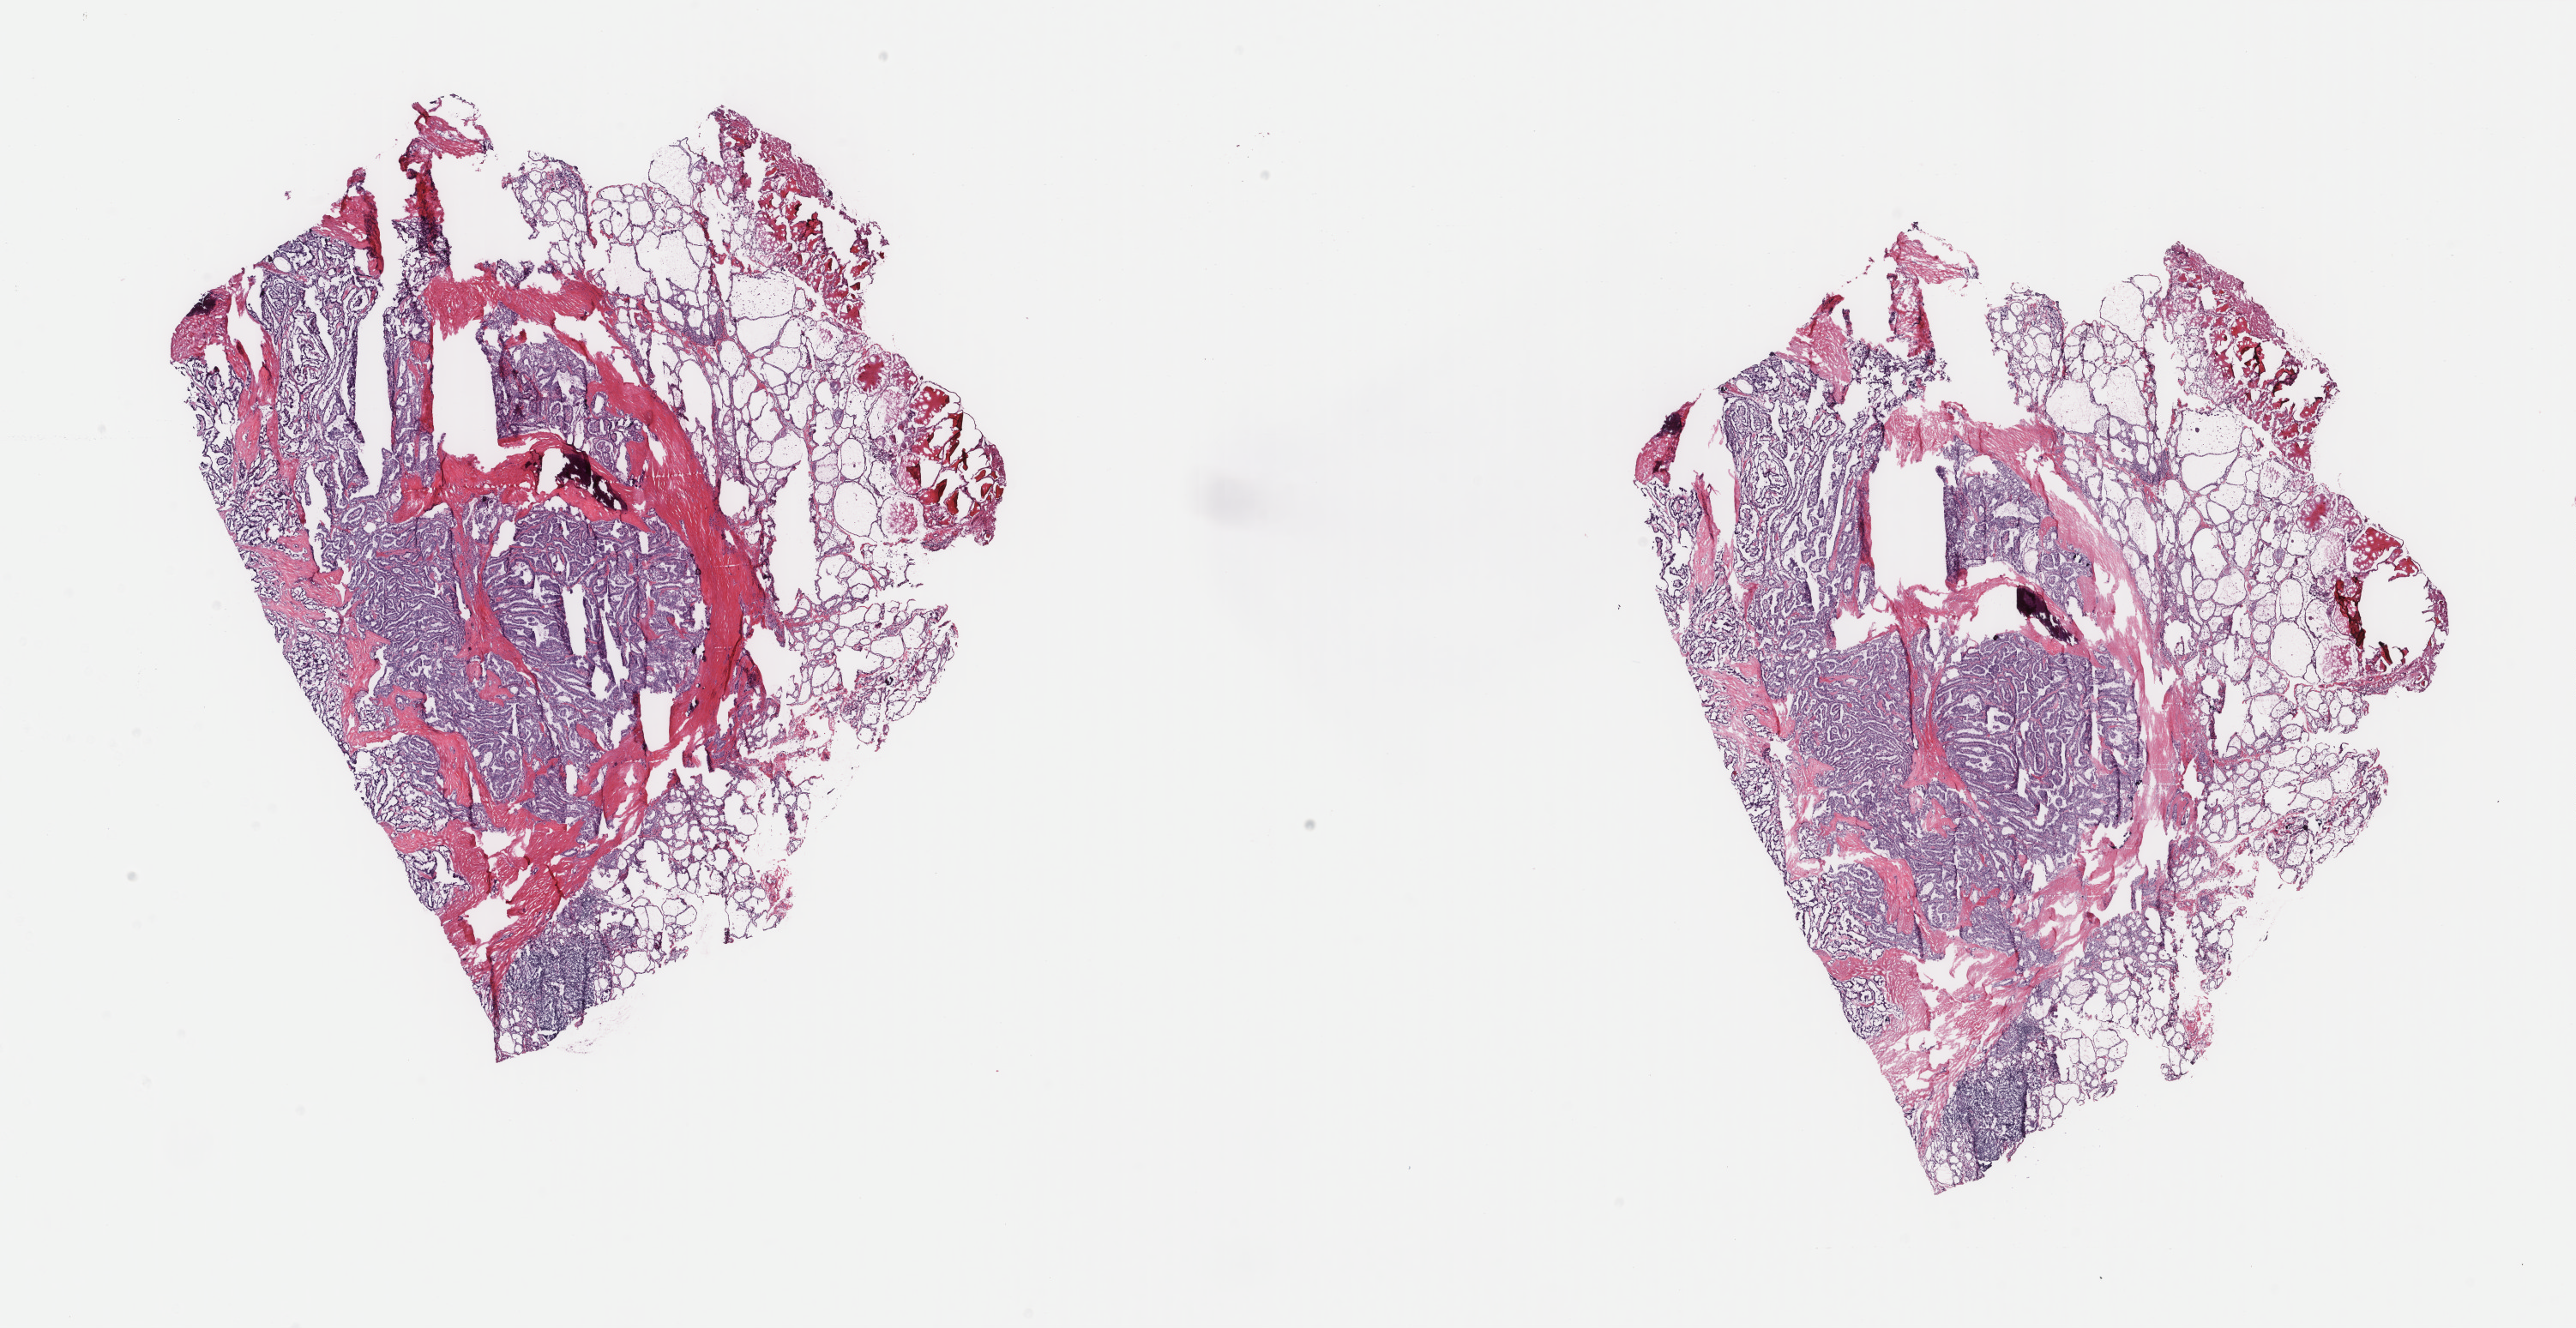
Whole-slide histology image, H&E-stained, shown as a low-resolution overview of the whole scanned area (about 23.8 x 12.3 mm, acquisition: 40x scan), frozen section from the top of the tissue portion, primary tumour sample from the thyroid. Female patient; age at initial diagnosis 40 years. Pathologist review of this section (percent, as recorded): tumour cells 60%, tumour nuclei 70%, normal cells 35%, stromal cells 5%, necrosis 0%. Infiltration values recorded for this section: lymphocyte infiltration 0%, monocyte infiltration 0%, neutrophil infiltration 0%.
* AJCC pathologic stage: I (7th edition)
* histologic diagnosis: Papillary adenocarcinoma, NOS (thyroid gland)